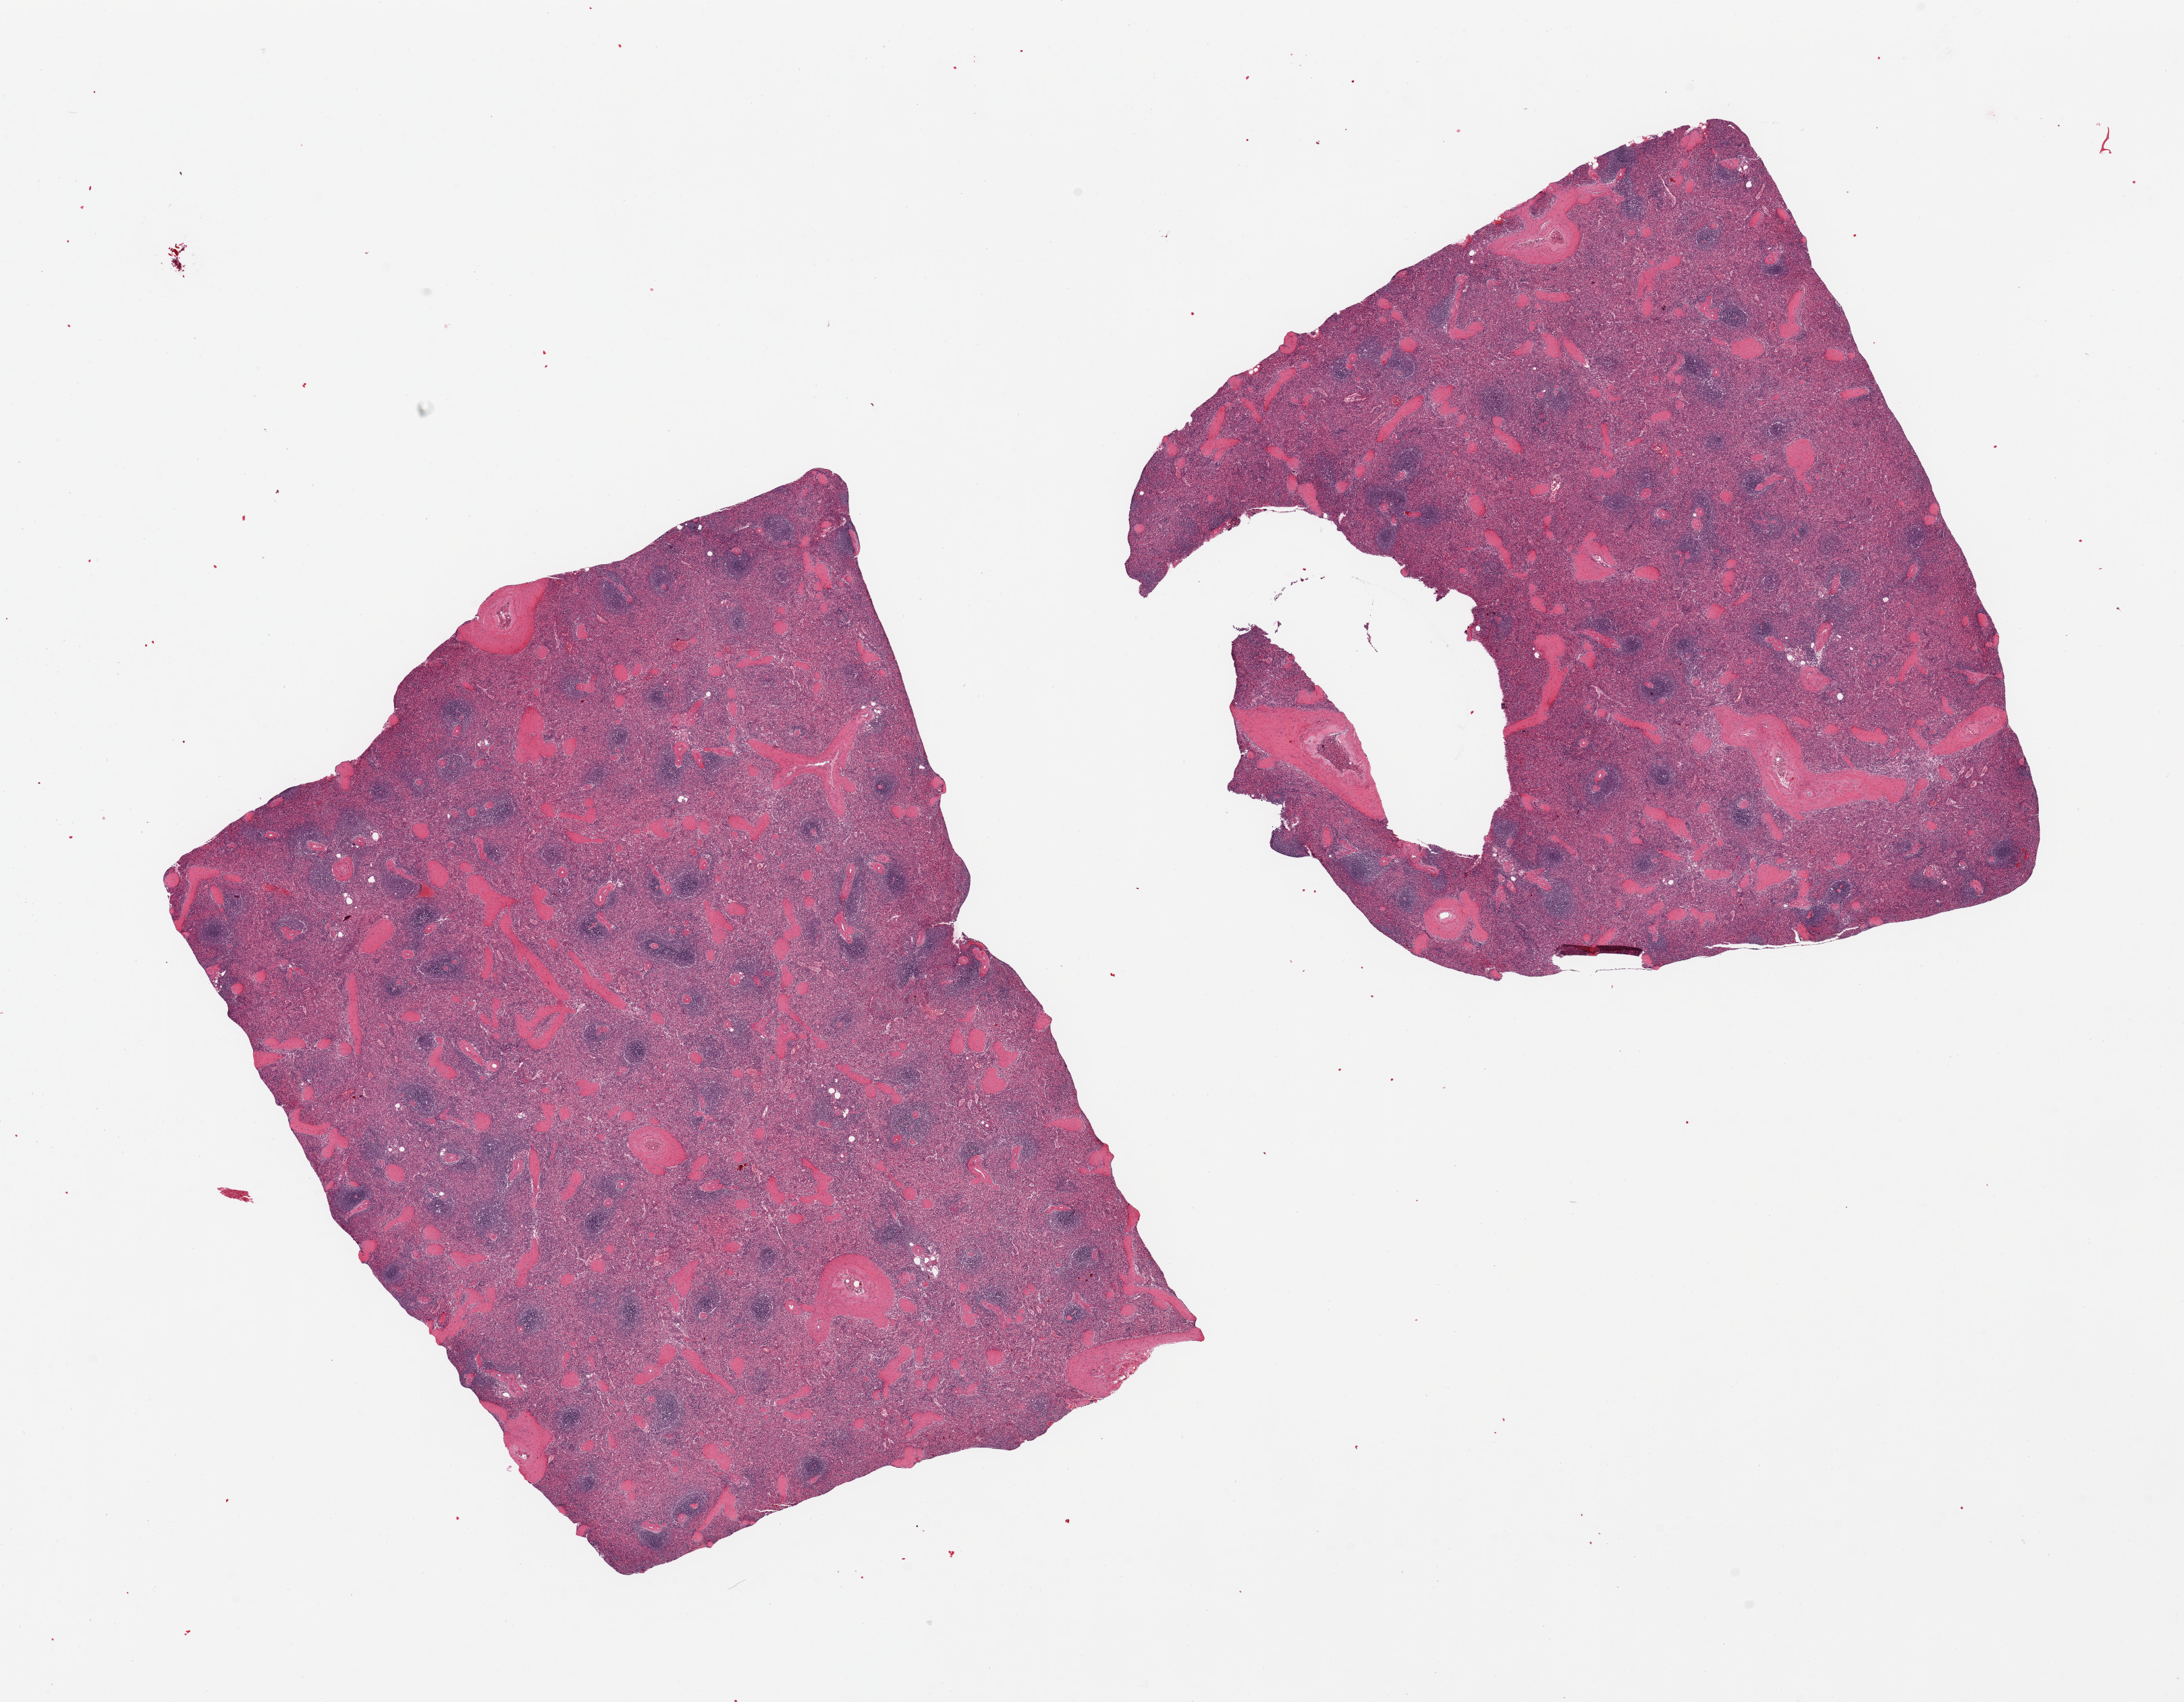
H&E whole-slide image, brightfield, a low-resolution overview of the entire scanned area, about 25.6 x 19.9 mm; PAXgene-fixed paraffin-embedded (PFPE) section; target tissue: spleen; donor tissue sample. Donor: male.
* reviewer comment on this tissue sample: 2 pieces